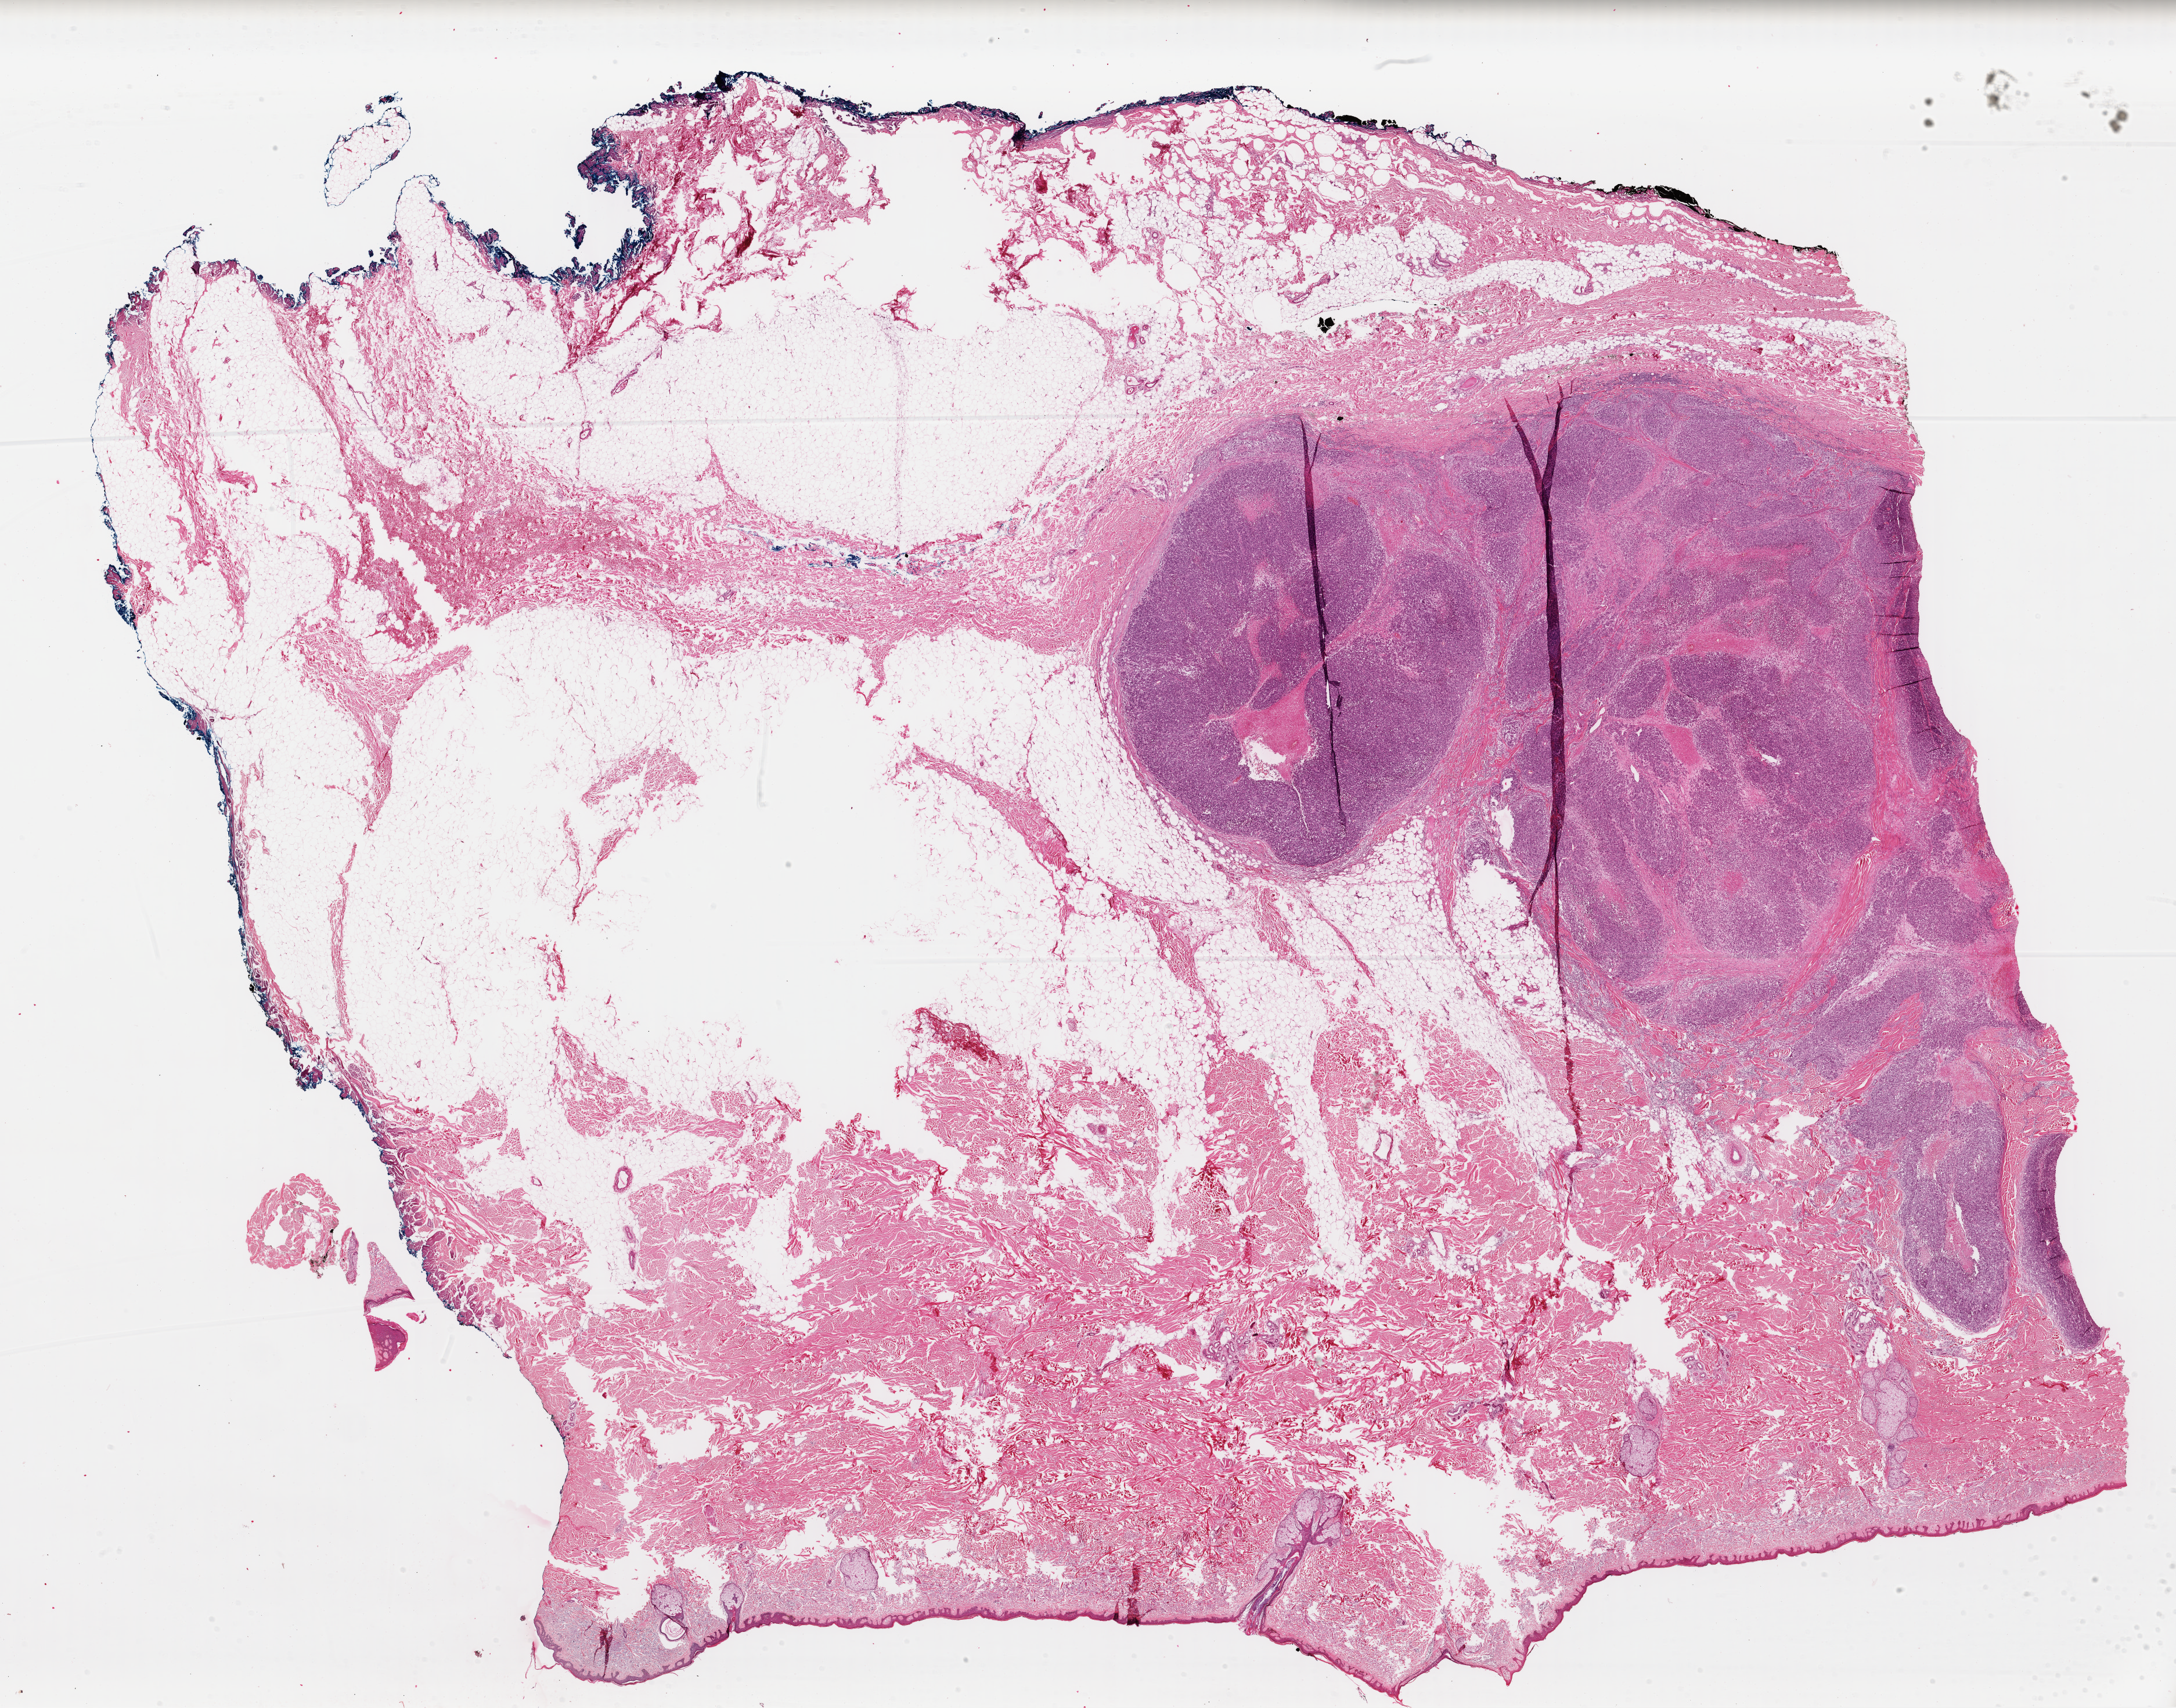
Digitized H&E tissue section (whole slide) — shown as a low-resolution overview of the whole scanned area (about 29.5 x 23.1 mm, slide scanned at 40x), FFPE section, primary tumour sample from the skin. Male patient; age at initial diagnosis 56 years.
* histologic diagnosis: Malignant melanoma, NOS